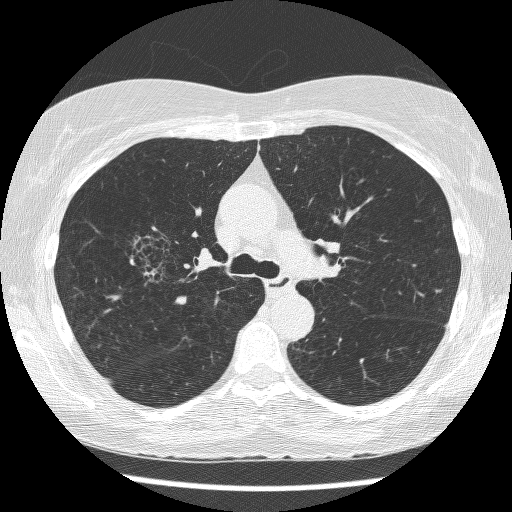
Low-dose screening chest CT, axial slice, baseline annual screen, lung window (W 1500 / L -600 HU), lung (sharp) reconstruction kernel (BONE). Female, age 64 years at enrolment.
• Expert-annotated lung lesion, box from (x=127, y=226) to (x=208, y=302) px.
• The screening reader recorded 3 non-calcified nodules or masses ≥4 mm on this exam (right upper lobe, right upper lobe, left lower lobe); which of them this box marks is not recorded.
• Official screen result: positive, change unspecified: nodule(s) >= 4 mm or enlarging nodule(s), mass(es), or other non-specific abnormalities suspicious for lung cancer.
• Lung cancer was diagnosed 735 days after this screen: adenocarcinoma, NOS, right upper lobe, right middle lobe, right hilum, stage IV (AJCC 6th edition), 85 mm at pathology.